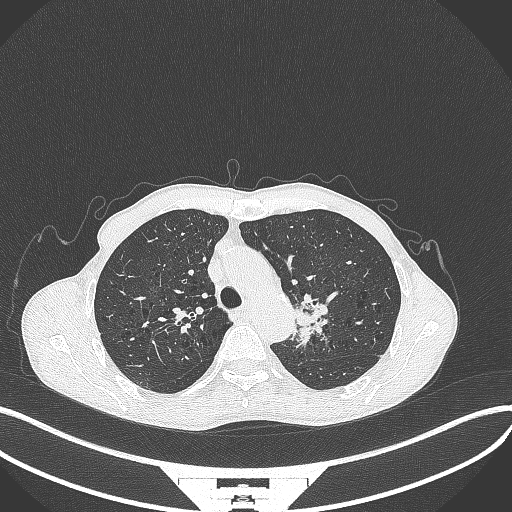
Chest CT, one axial slice; reconstruction kernel B70f; 120 kVp; lung window (W 1500 / L -600 HU); 512 × 512 image matrix. Patient: male, 65 years. From the clinical record (not read from this slice): clinical TNM (as recorded): T2b N0 M0.
Annotated regions visible in this slice (bounding box drawn by a radiologist):
- lung tumour (recorded histology: adenocarcinoma): bounding box [x1, y1, x2, y2] px = [291, 289, 330, 355]